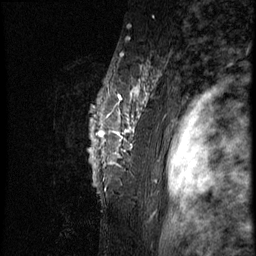
Breast MRI (dynamic contrast-enhanced), one sagittal slice; slice 61 of 66 in the series (ordered by position); 3 images stored at this slice position (order not interpretable as contrast timing); 1.5 T; TE 4.2 ms, TR 8.9 ms; 2.5 mm slice thickness; 256 × 256 image matrix, field of view 200 × 200 mm. Patient: female, 39 years. Case-level facts recorded for this patient, not image findings: setting: breast cancer imaged before/during neoadjuvant chemotherapy; receptor status: HER2-positive.
Annotated regions visible in this slice (semi-automatic segmentation, software-assisted and operator-edited):
- analysis volume of interest (the breast-tissue region the enhancement analysis was run in; not a lesion): box from (x=54, y=49) to (x=166, y=196) px
- tumour enhancement mask (voxels above the 140 % enhancement threshold inside the analysis volume of interest): (x=99, y=85)–(x=139, y=139)